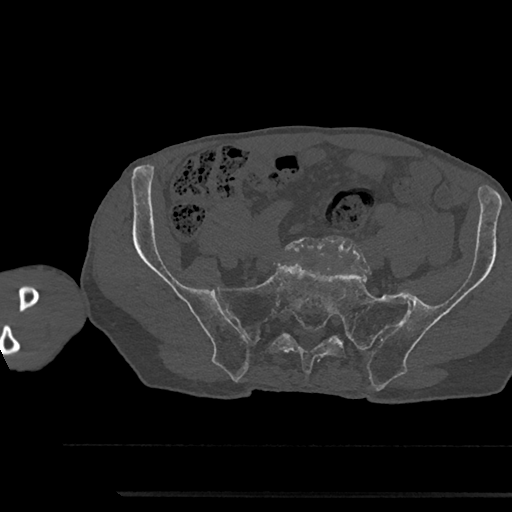
CT including the spine, one axial slice. Position 287 of 797 along the scan axis. Reconstruction kernel Br40s/3. 120 kVp. Bone window (W 1800 / L 400 HU). 0.5 mm slice thickness. 512 × 512 image matrix, field of view 367 × 367 mm. Patient: male, 79 years. From the clinical record (not read from this slice): primary cancer: prostate.
Structures marked on this image (semi-automatically segmented with operator editing):
- L5 vertebra: bounding box [x1, y1, x2, y2] px = [285, 238, 358, 265]